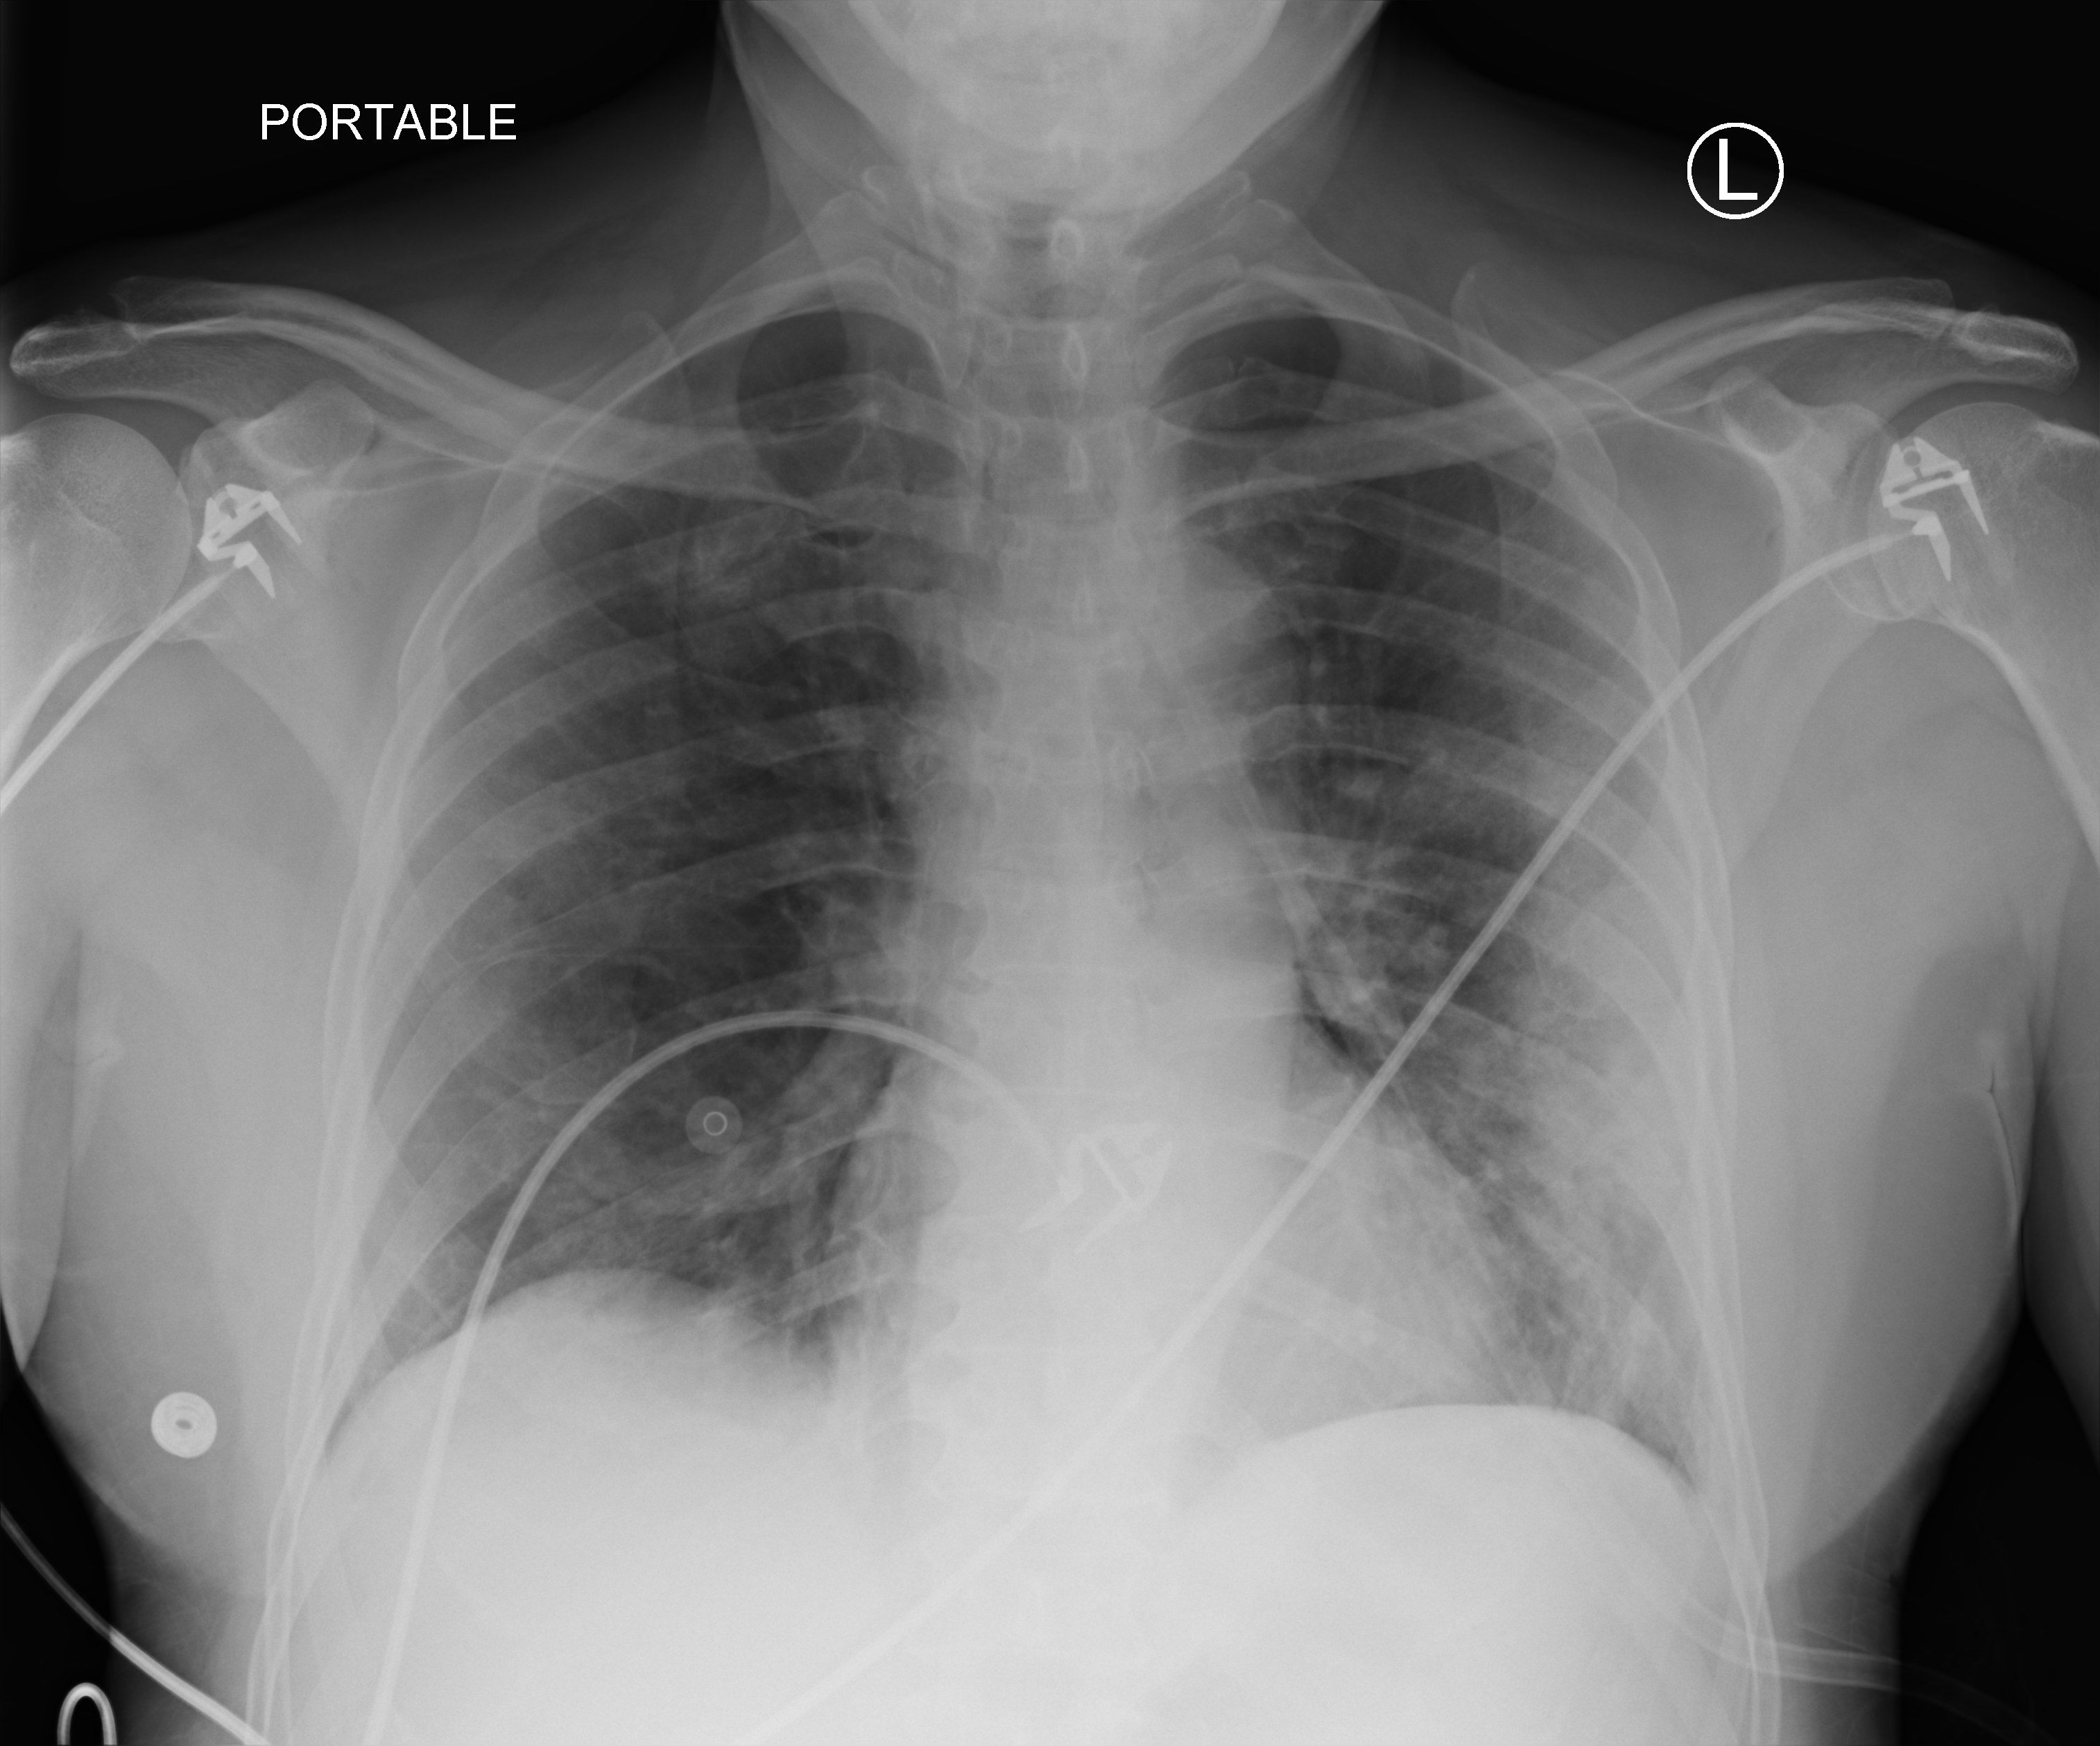
Chest X-ray (portable), anteroposterior (AP) projection. Patient hospitalised with COVID-19; male, aged 60–74 years.
Admission-level facts for this patient (not findings on this image; timing relative to this image not recorded):
- other chronic lung disease (admission record): no